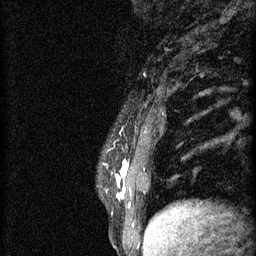
Breast MRI (dynamic contrast-enhanced), one sagittal slice. Slice 15 of 60 in the series (ordered by position). 3 images stored at this slice position (order not interpretable as contrast timing). 1.5 T. TE 4.2 ms, TR 11 ms. 256 × 256 image matrix. Patient: female, 37 years.
Annotated regions visible in this slice (semi-automatic segmentation, software-assisted and operator-edited):
- analysis volume of interest (the breast-tissue region the enhancement analysis was run in; not a lesion): bounding box [x1, y1, x2, y2] px = [116, 142, 173, 221]
- tumour enhancement mask (voxels above the 70 % enhancement threshold inside the analysis volume of interest): [116, 160, 128, 201]